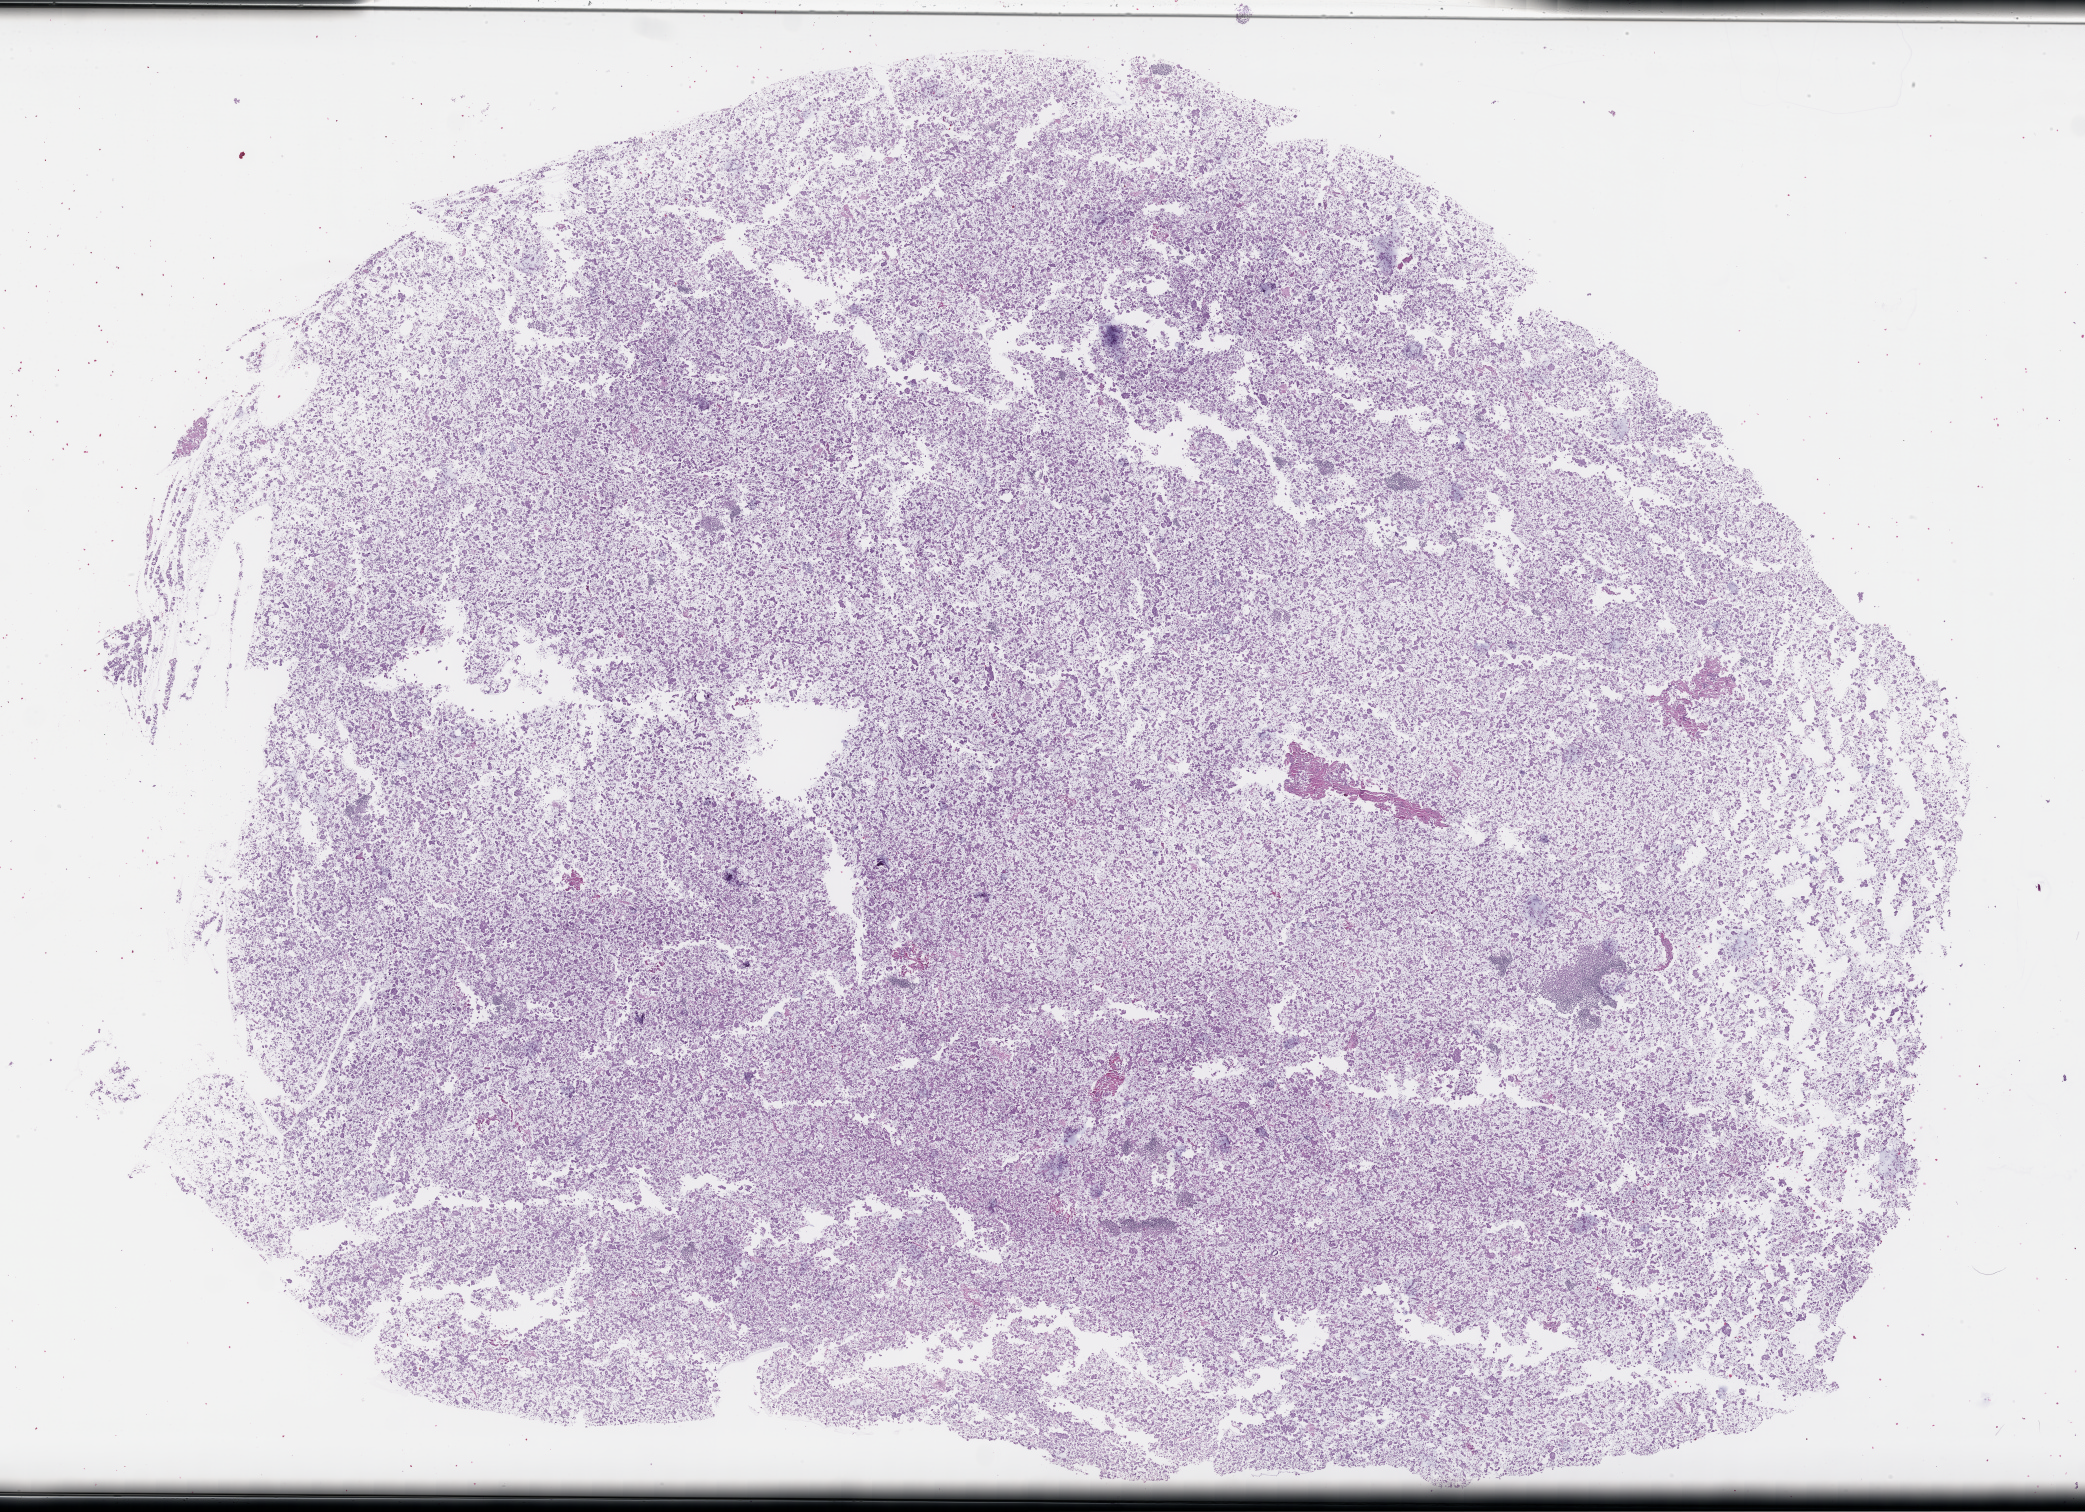
H&E whole-slide image — low-resolution overview of the scanned area, about 33.7 x 24.4 mm; FFPE section; site: ovary. Patient: female.
- this section: primary tumor
- diagnosis: Ovarian Carcinoma